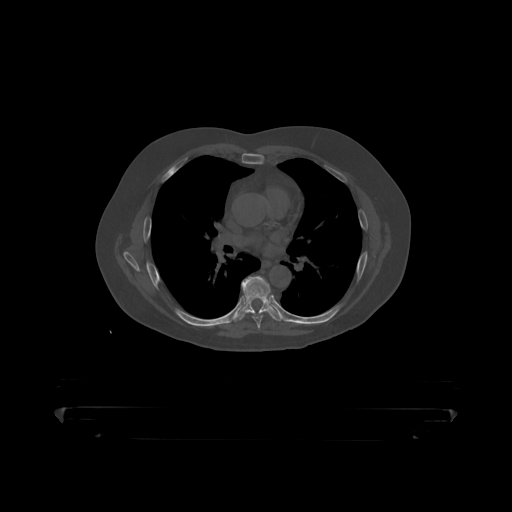
CT including the spine, one axial slice; position 288 of 390 along the scan axis; reconstruction kernel STANDARD; 120 kVp; bone window (W 1800 / L 400 HU); 1.25 mm slice thickness; 512 × 512 image matrix, field of view 650 × 650 mm. Male patient, age 60 years. Case-level facts recorded for this patient, not image findings: primary cancer: prostate.
Annotated regions visible in this slice (semi-automatic segmentation, software-assisted and operator-edited):
- T6 vertebra: bounding box (x1, y1, x2, y2) in pixels: (253, 314, 263, 319)
- T7 vertebra: (239, 277, 280, 318)